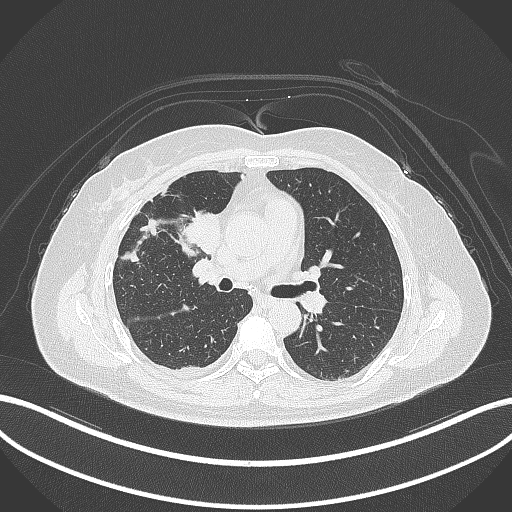
Chest CT, one axial slice. Position 159 of 305 along the scan axis. Reconstruction kernel B70f. 120 kVp. Lung window (W 1500 / L -600 HU). 512 × 512 image matrix, field of view 400 × 400 mm. Patient: female, 52 years. Case-level facts recorded for this patient, not image findings: clinical TNM (as recorded): T3 N1 M1.
Outlined on this slice (rectangle marked by the reading radiologist):
- lung tumour (recorded histology: adenocarcinoma): bounding box <181,204,223,254> (left, top, right, bottom; pixels)